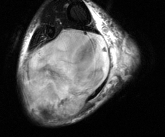
MRI of an extremity soft-tissue mass, one axial slice; position 38 of 81 along the scan axis; T2-weighted fat-saturated; MR volume resampled by the dataset authors to the PET/CT grid (not the native acquisition matrix); 165 × 137 image matrix, field of view 161 × 134 mm. Male patient. Case-level facts recorded for this patient, not image findings: histological type: liposarcoma - round cell; grade: high; site of the primary tumour: right calf.
Outlined on this slice (expert contour drawn on MRI and transferred to this co-registered scan by the dataset authors):
- gross tumour volume (mass): bounding box [x1, y1, x2, y2] px = [23, 29, 111, 117]